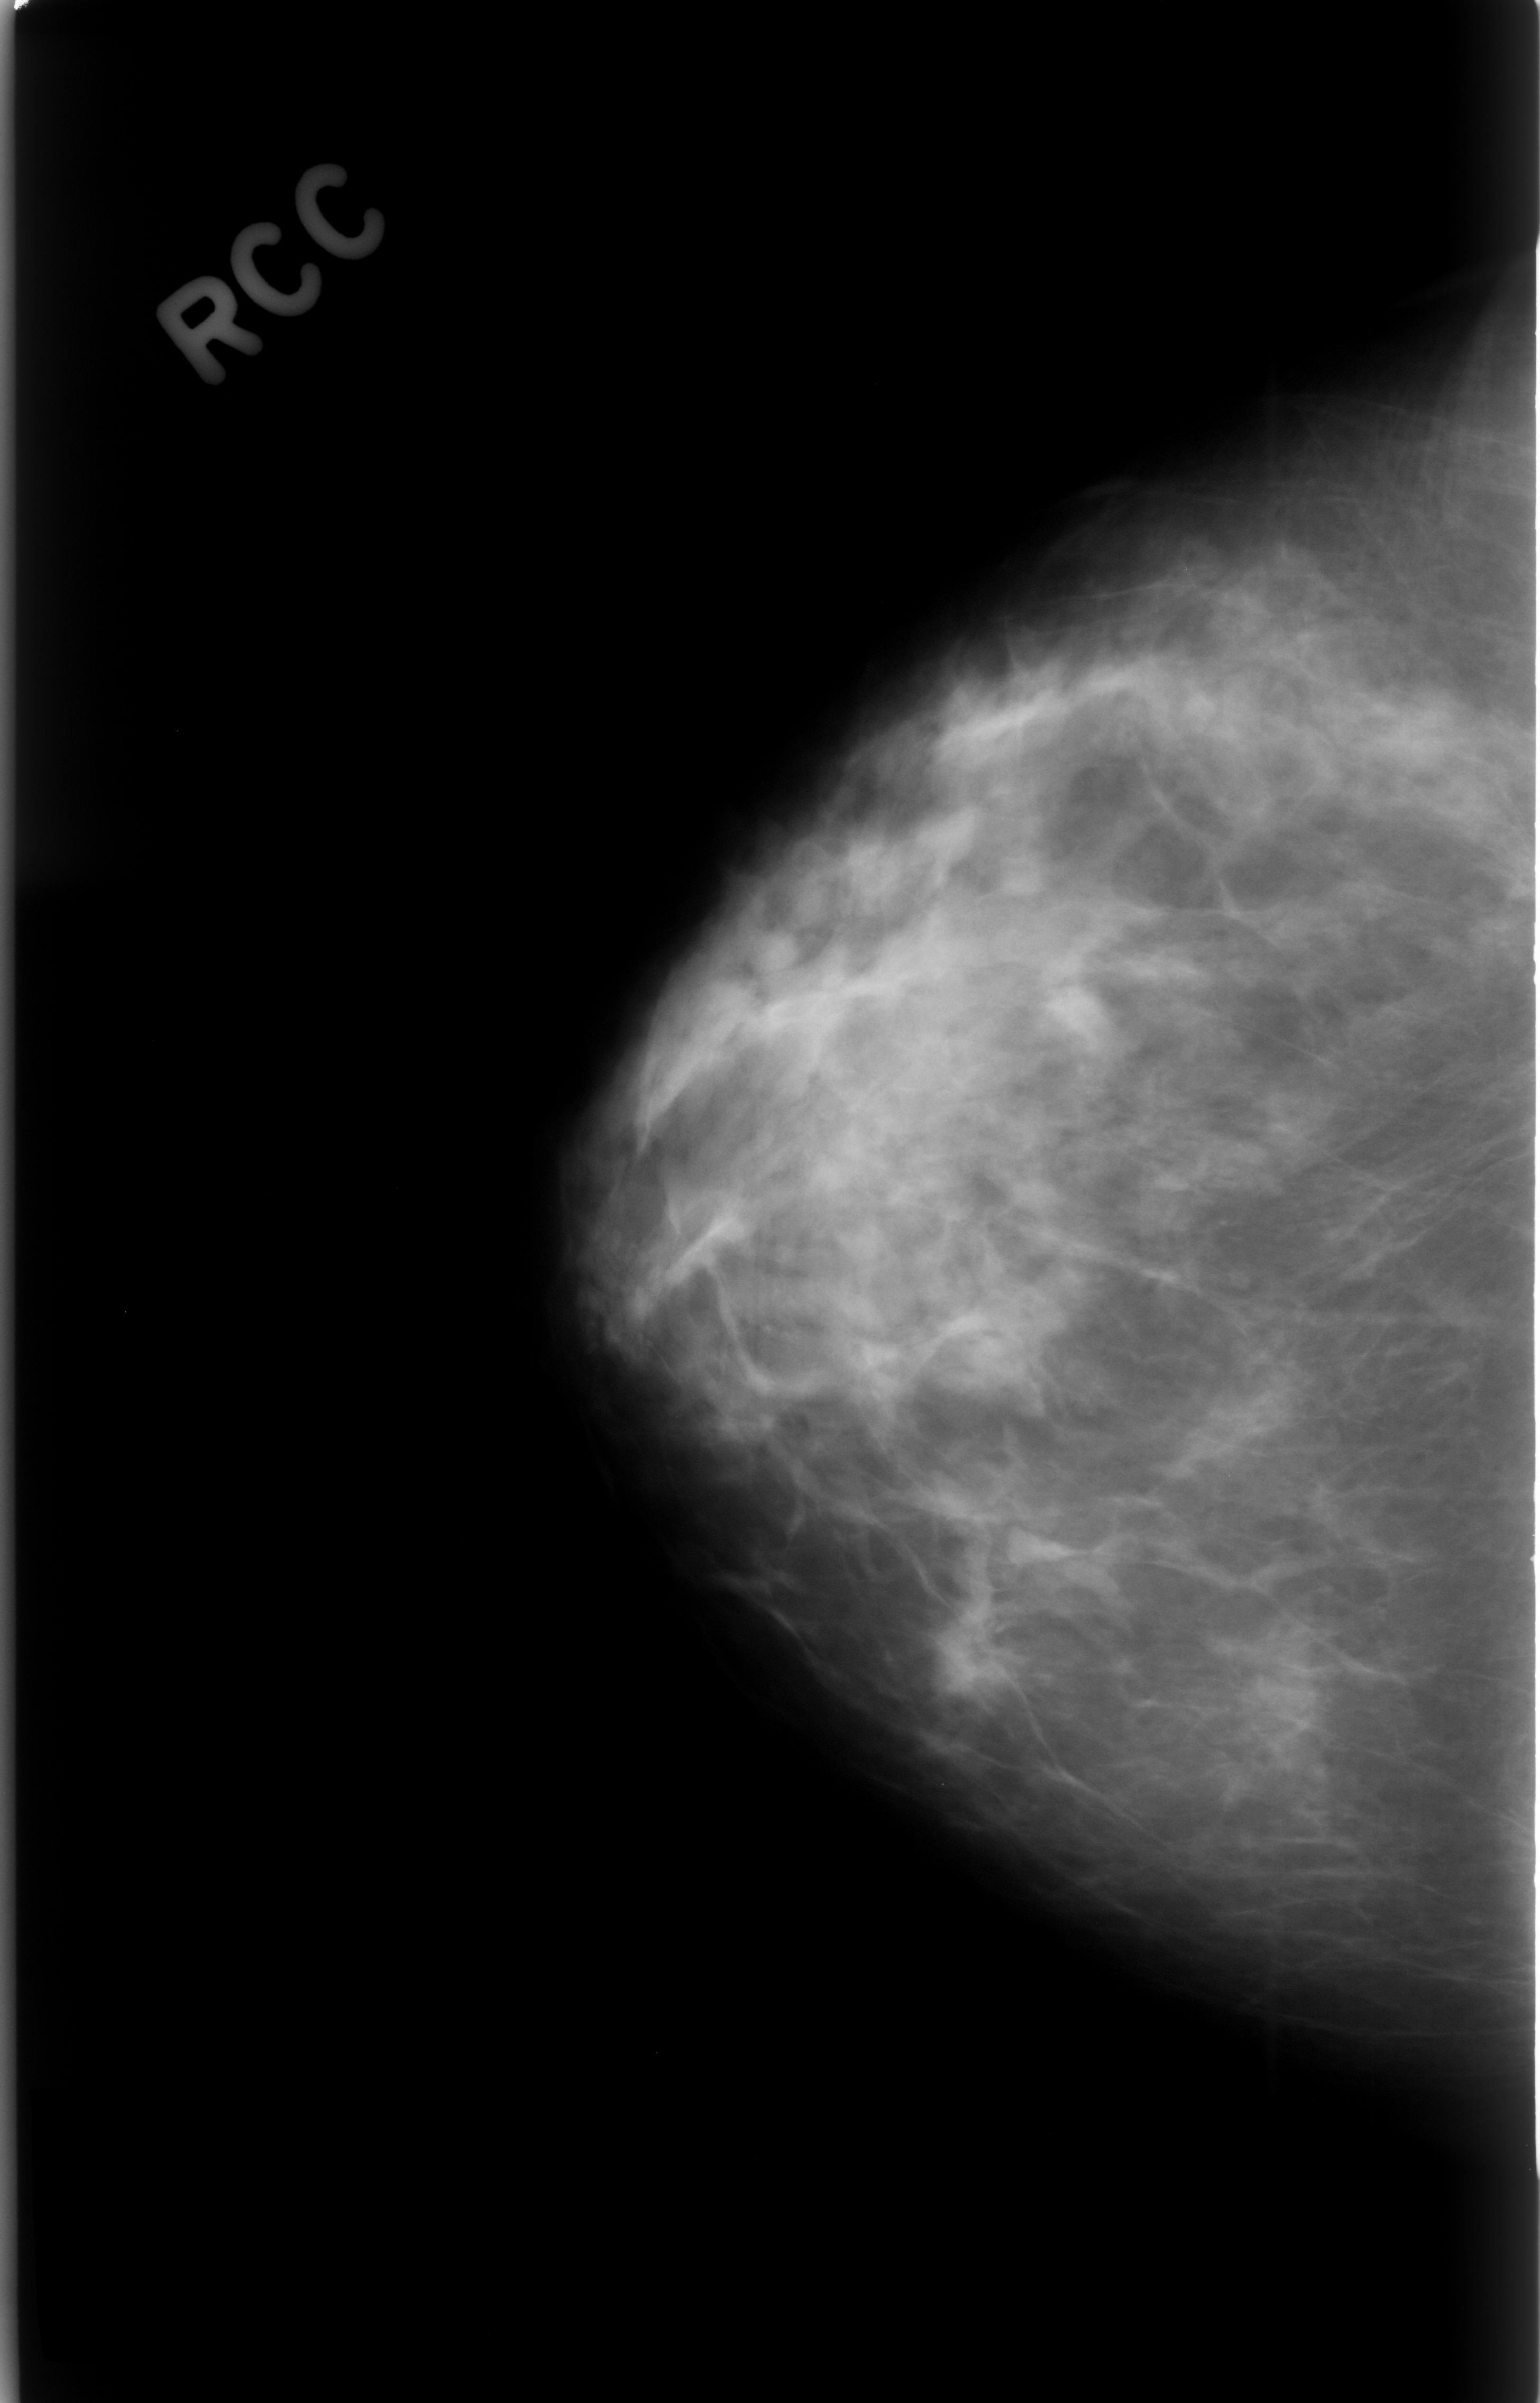
Mammogram (digitized film); right breast; craniocaudal (CC) view; BI-RADS breast density category 2 (scale 1–4); 1540 × 2403 image matrix.
Marked abnormalities (boxes around the expert regions of interest):
- mass, shape irregular, margins spiculated; BI-RADS assessment category 3; outcome (as recorded, no biopsy): benign without callback (not worked up further): bounding box (x1, y1, x2, y2) in pixels: (914, 1547, 1051, 1715)